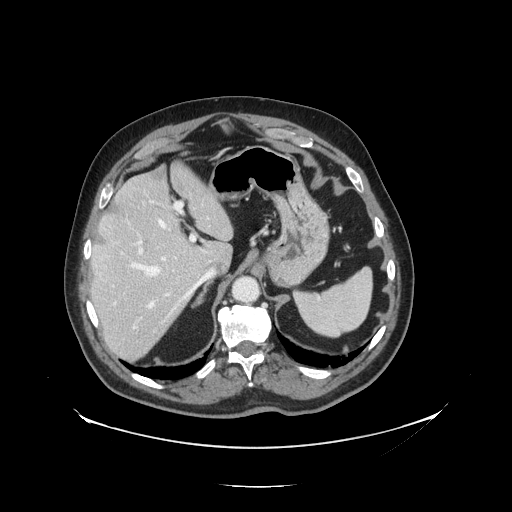
Contrast-enhanced abdominal CT, one axial slice; position 97 of 138 along the scan axis; 120 kVp; intravenous contrast given; soft-tissue window (W 400 / L 40 HU); 2.5 mm slice thickness; 512 × 512 image matrix, field of view 497 × 497 mm. Male patient, age 77 years. From the clinical record (not read from this slice): diagnosis: colorectal cancer liver metastases, imaged before liver resection; multiple liver metastases: no; largest metastasis: 1.5 cm; disease in both lobes: no.
Outlined on this slice (outlined manually by an expert reader):
- hepatic veins: bounding box [x1, y1, x2, y2] px = [131, 219, 210, 314]
- liver: [91, 167, 233, 361]
- planned liver remnant (the part of the liver to remain after resection): [92, 166, 233, 288]
- portal vein (with intrahepatic branches): [116, 202, 210, 309]